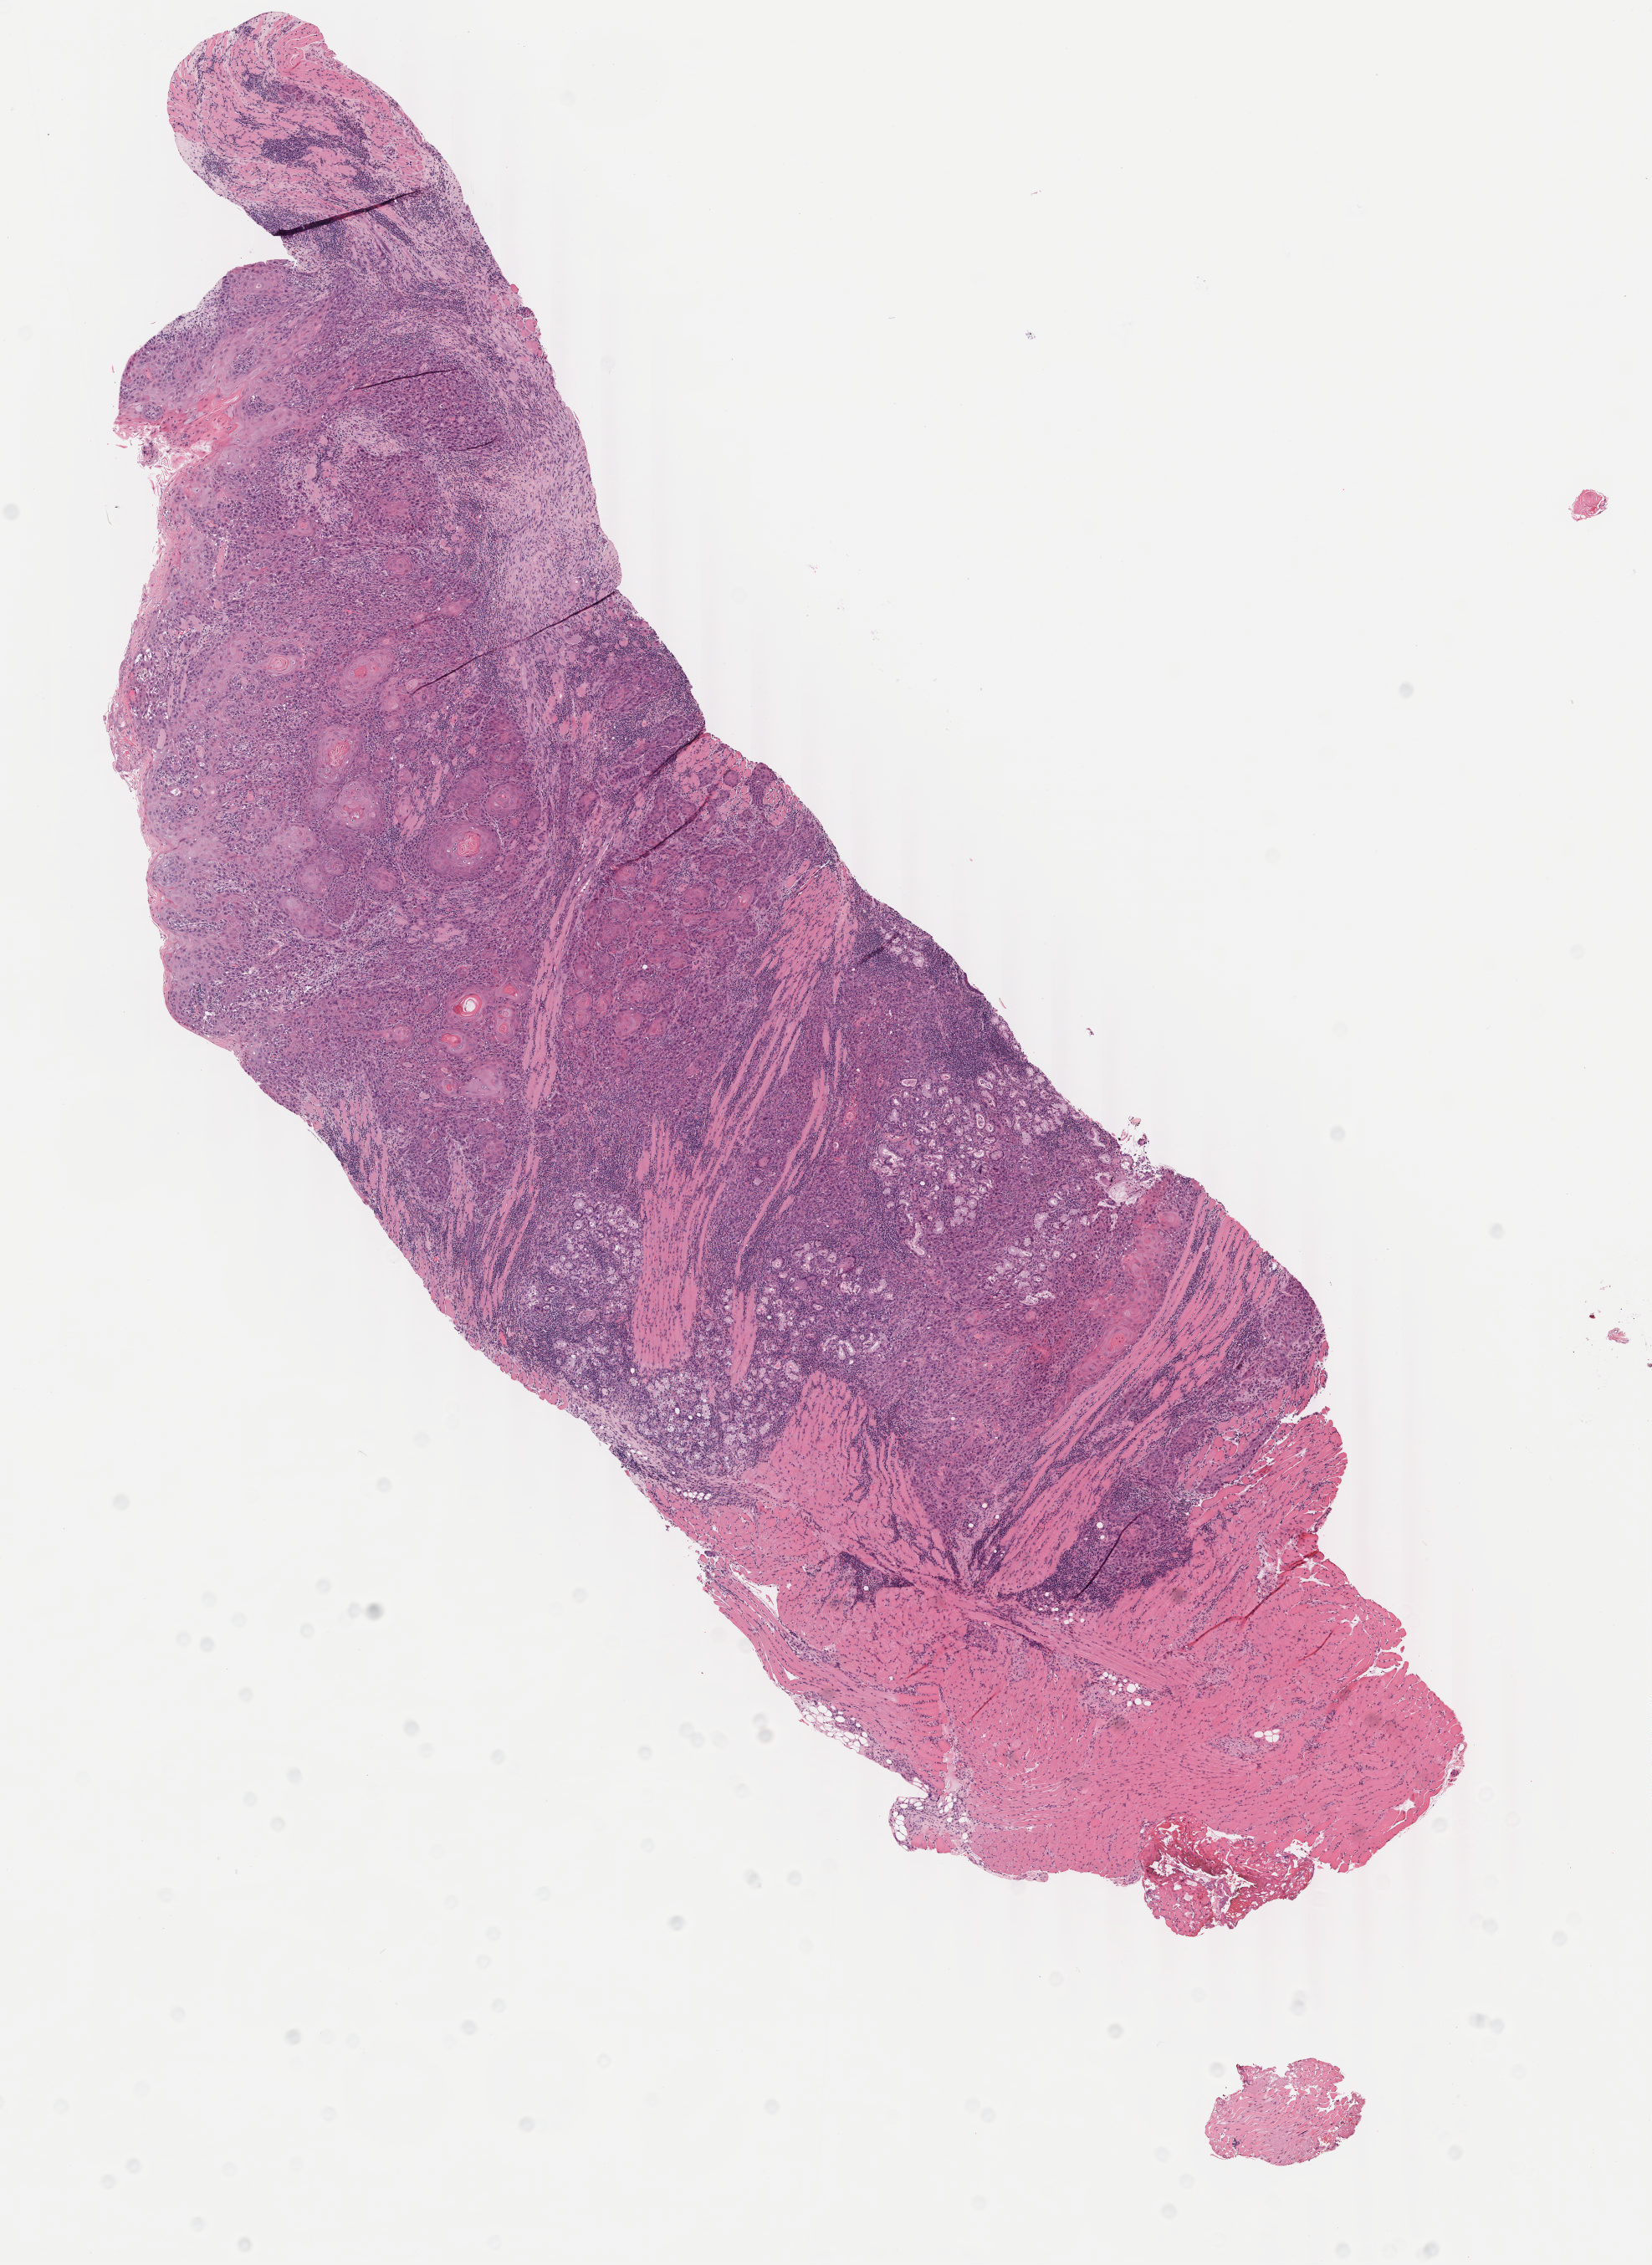
Digitized Hematoxylin and eosin (H&E) stained tissue section (whole slide) — whole scanned area (about 7.9 x 10.8 mm) shown as a low-resolution overview. Formalin-fixed paraffin-embedded (FFPE) diagnostic section. Head and neck, primary tumour sample. Female patient; age at initial diagnosis 35 years. Histologic grade: G2 (moderately differentiated).
* diagnosis: Squamous cell carcinoma, keratinizing, NOS (tongue, NOS)
* AJCC pathologic stage: IVA (7th edition)